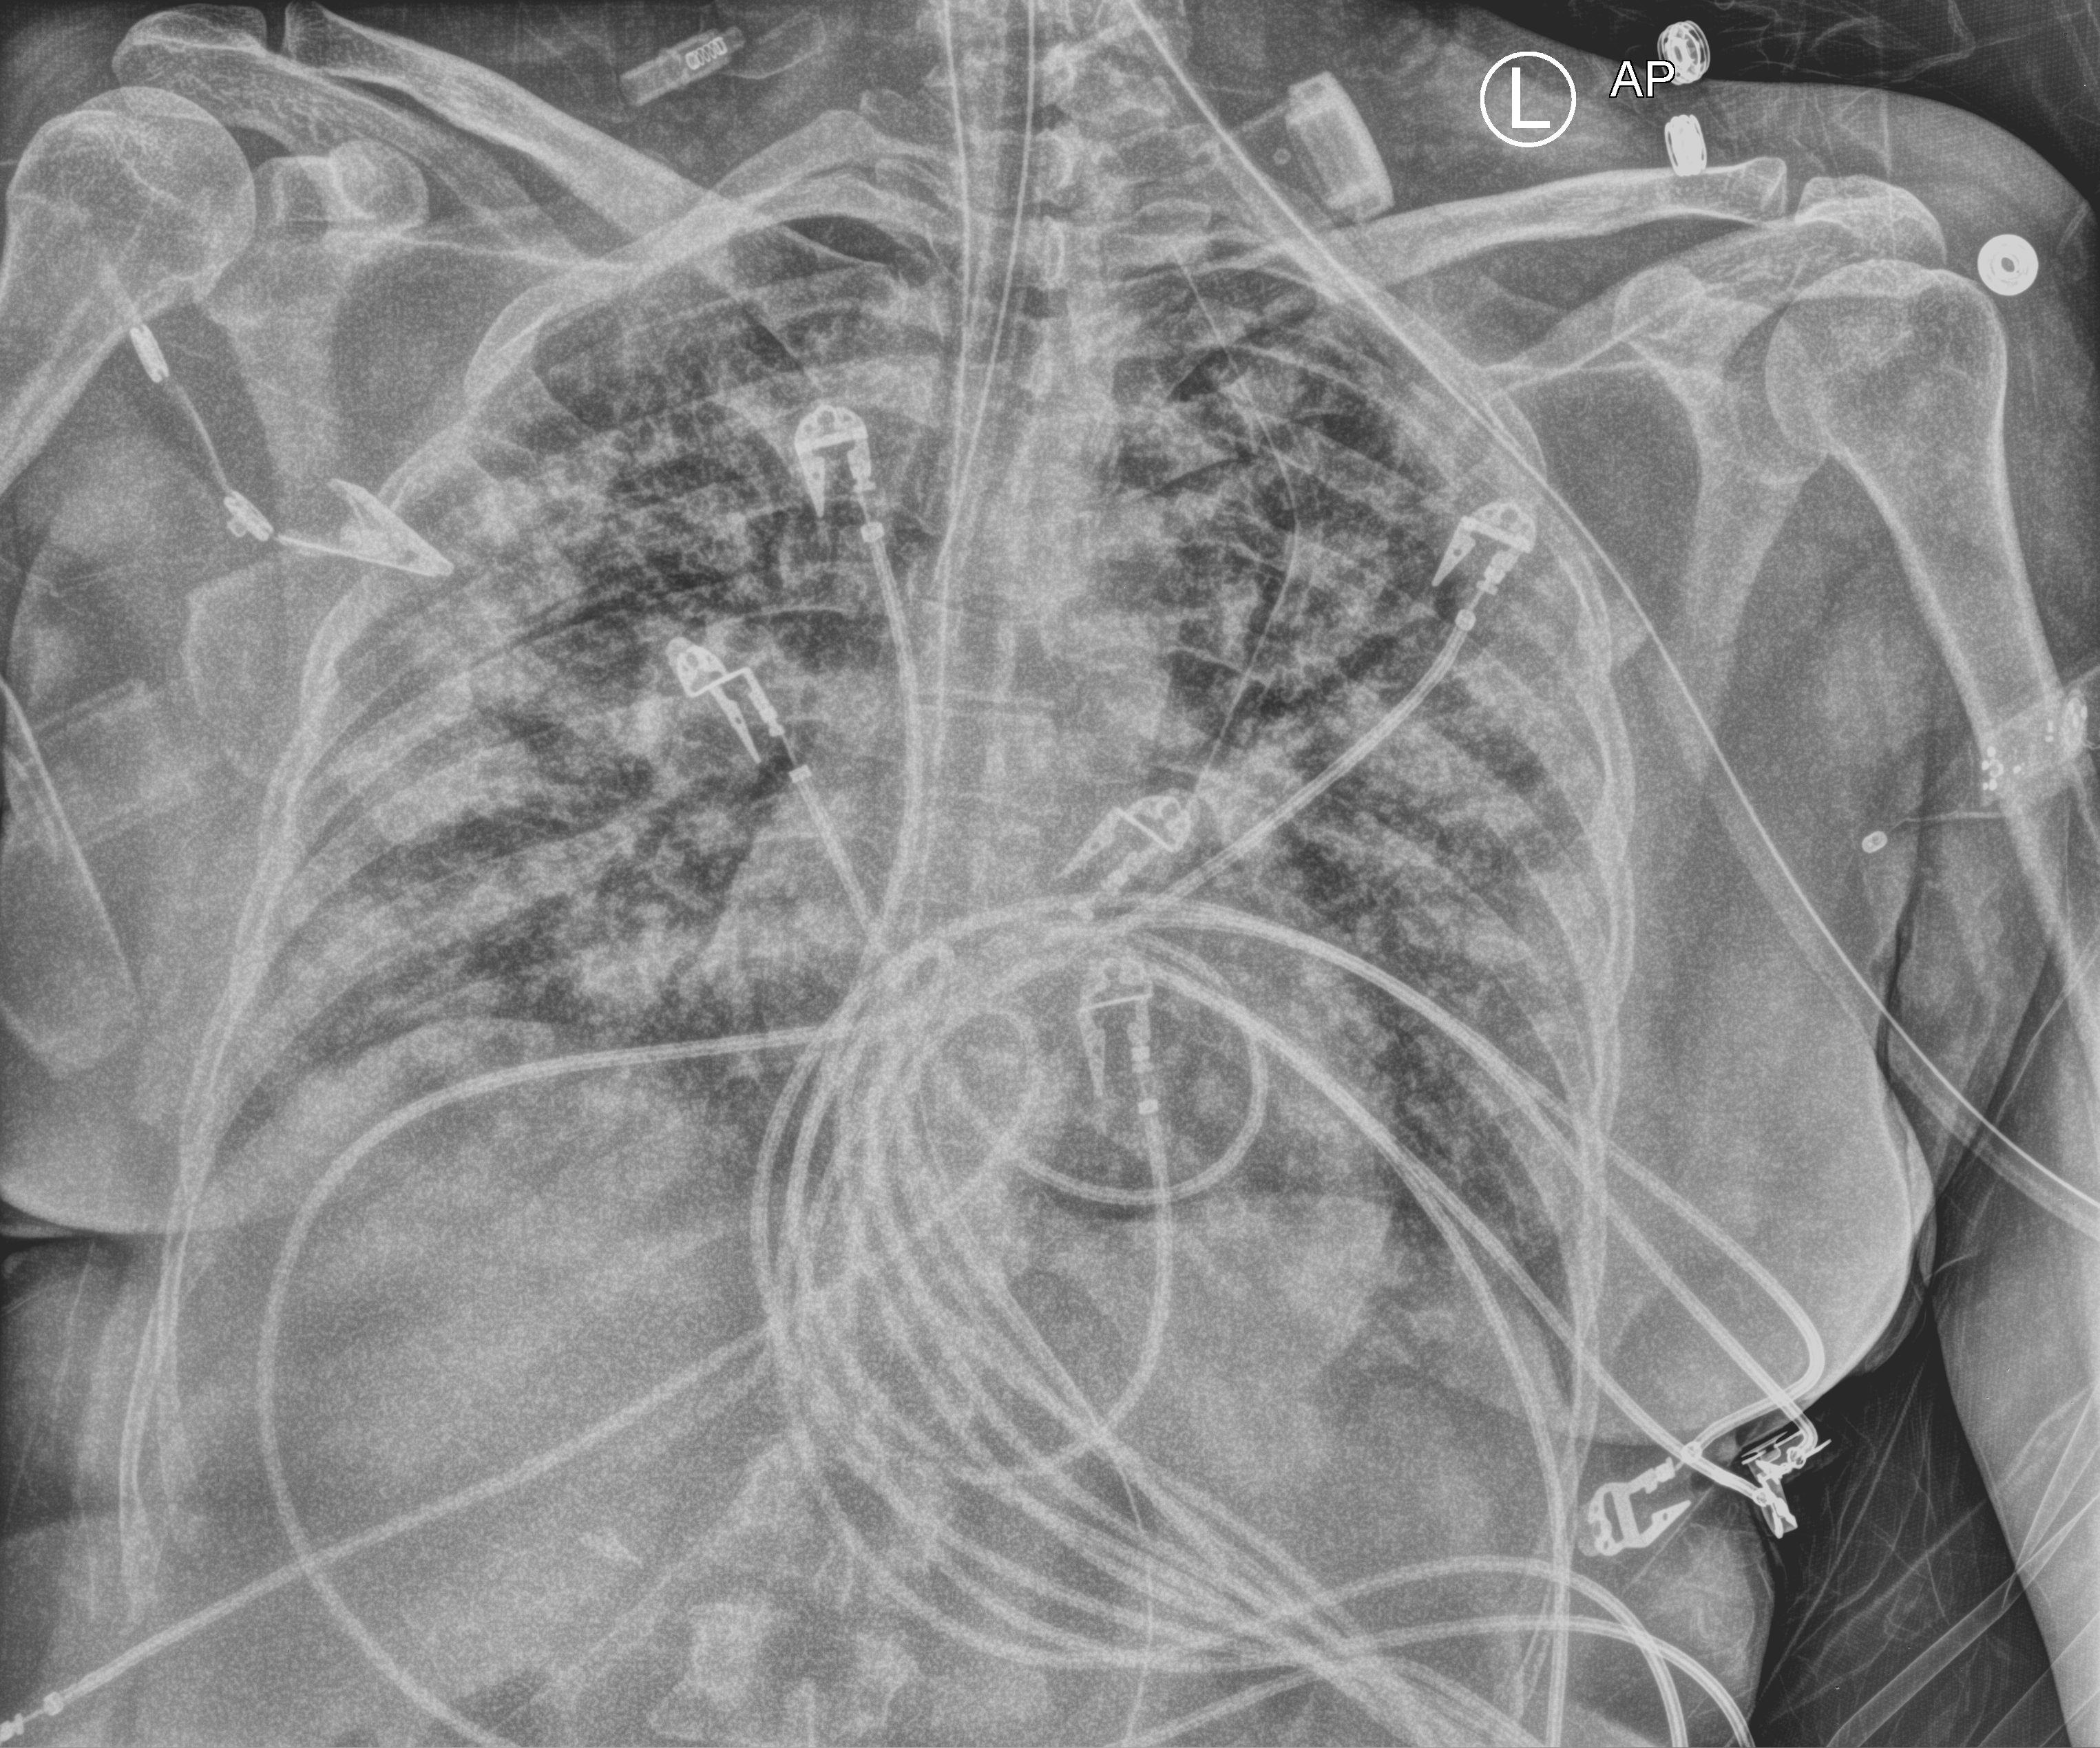
Chest X-ray (portable), anteroposterior (AP) projection. Female patient hospitalised with COVID-19, age 18–59 years.
From the hospital-stay record, not from the radiograph (when in the stay this image was taken is not recorded): admitted to intensive care during this hospital stay: yes.